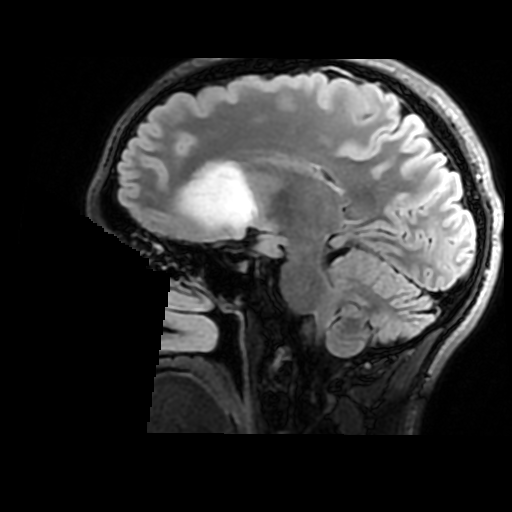
Brain MRI from a brain-tumour surgery series, one sagittal slice; position 100 of 176 along the scan axis; T2 FLAIR; 512 × 512 image matrix. Case-level facts recorded for this patient, not image findings: histopathology: Astrocytoma; WHO grade: 2; IDH mutation: yes.
Outlined on this slice (expert manual segmentation):
- tumour: bounding box [x1, y1, x2, y2] px = [182, 164, 256, 230]